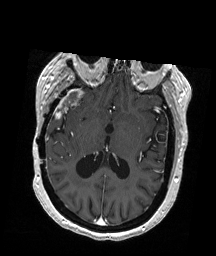
Brain MRI from a brain-tumour surgery series, one axial slice; slice 99 of 192 in the series (ordered by position); T1-weighted post-contrast; 1 mm slice thickness; 216 × 256 image matrix, field of view 211 × 250 mm. Case-level facts recorded for this patient, not image findings: histopathology: Glioblastoma; WHO grade: 4; IDH mutation: no; tumour location: Right Temporal.
Annotated regions visible in this slice (outlined manually by an expert reader):
- tumour: bounding box (x1, y1, x2, y2) in pixels: (56, 89, 83, 117)